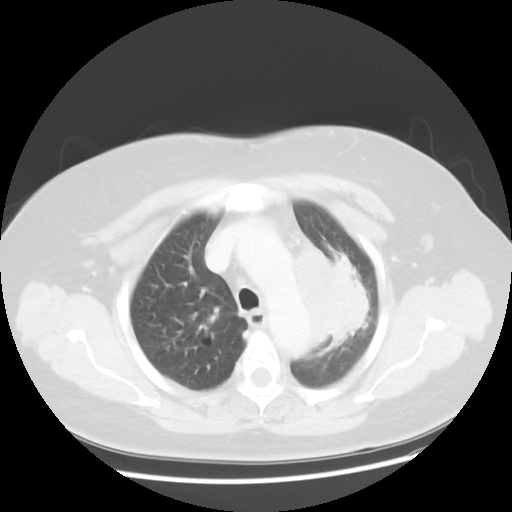
Chest CT, one axial slice. Slice 36 of 49 in the series (ordered by position). Reconstruction kernel STANDARD. Lung window (W 1500 / L -600 HU). 512 × 512 image matrix, field of view 374 × 374 mm. Patient: female, 58 years. From the clinical record (not read from this slice): clinical TNM (as recorded): T4 N3 M0; histopathological grade: G3.
Structures marked on this image (bounding box drawn by a radiologist):
- lung tumour (recorded histology: small cell carcinoma): box from (x=292, y=232) to (x=379, y=348) px